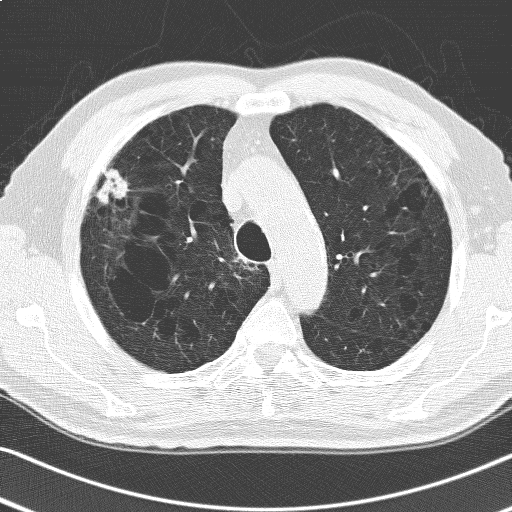
Low-dose screening chest CT, one axial slice. Slice 130 of 168 in the series (ordered by position). 120 kVp. Lung window (W 1500 / L -600 HU). 3.2 mm slice thickness. 512 × 512 image matrix, field of view 336 × 336 mm.
Outlined on this slice (outlined manually by an expert reader):
- lesion 1 (tumor, upper lobe of right lung): bounding box (x1, y1, x2, y2) in pixels: (95, 168, 128, 205)